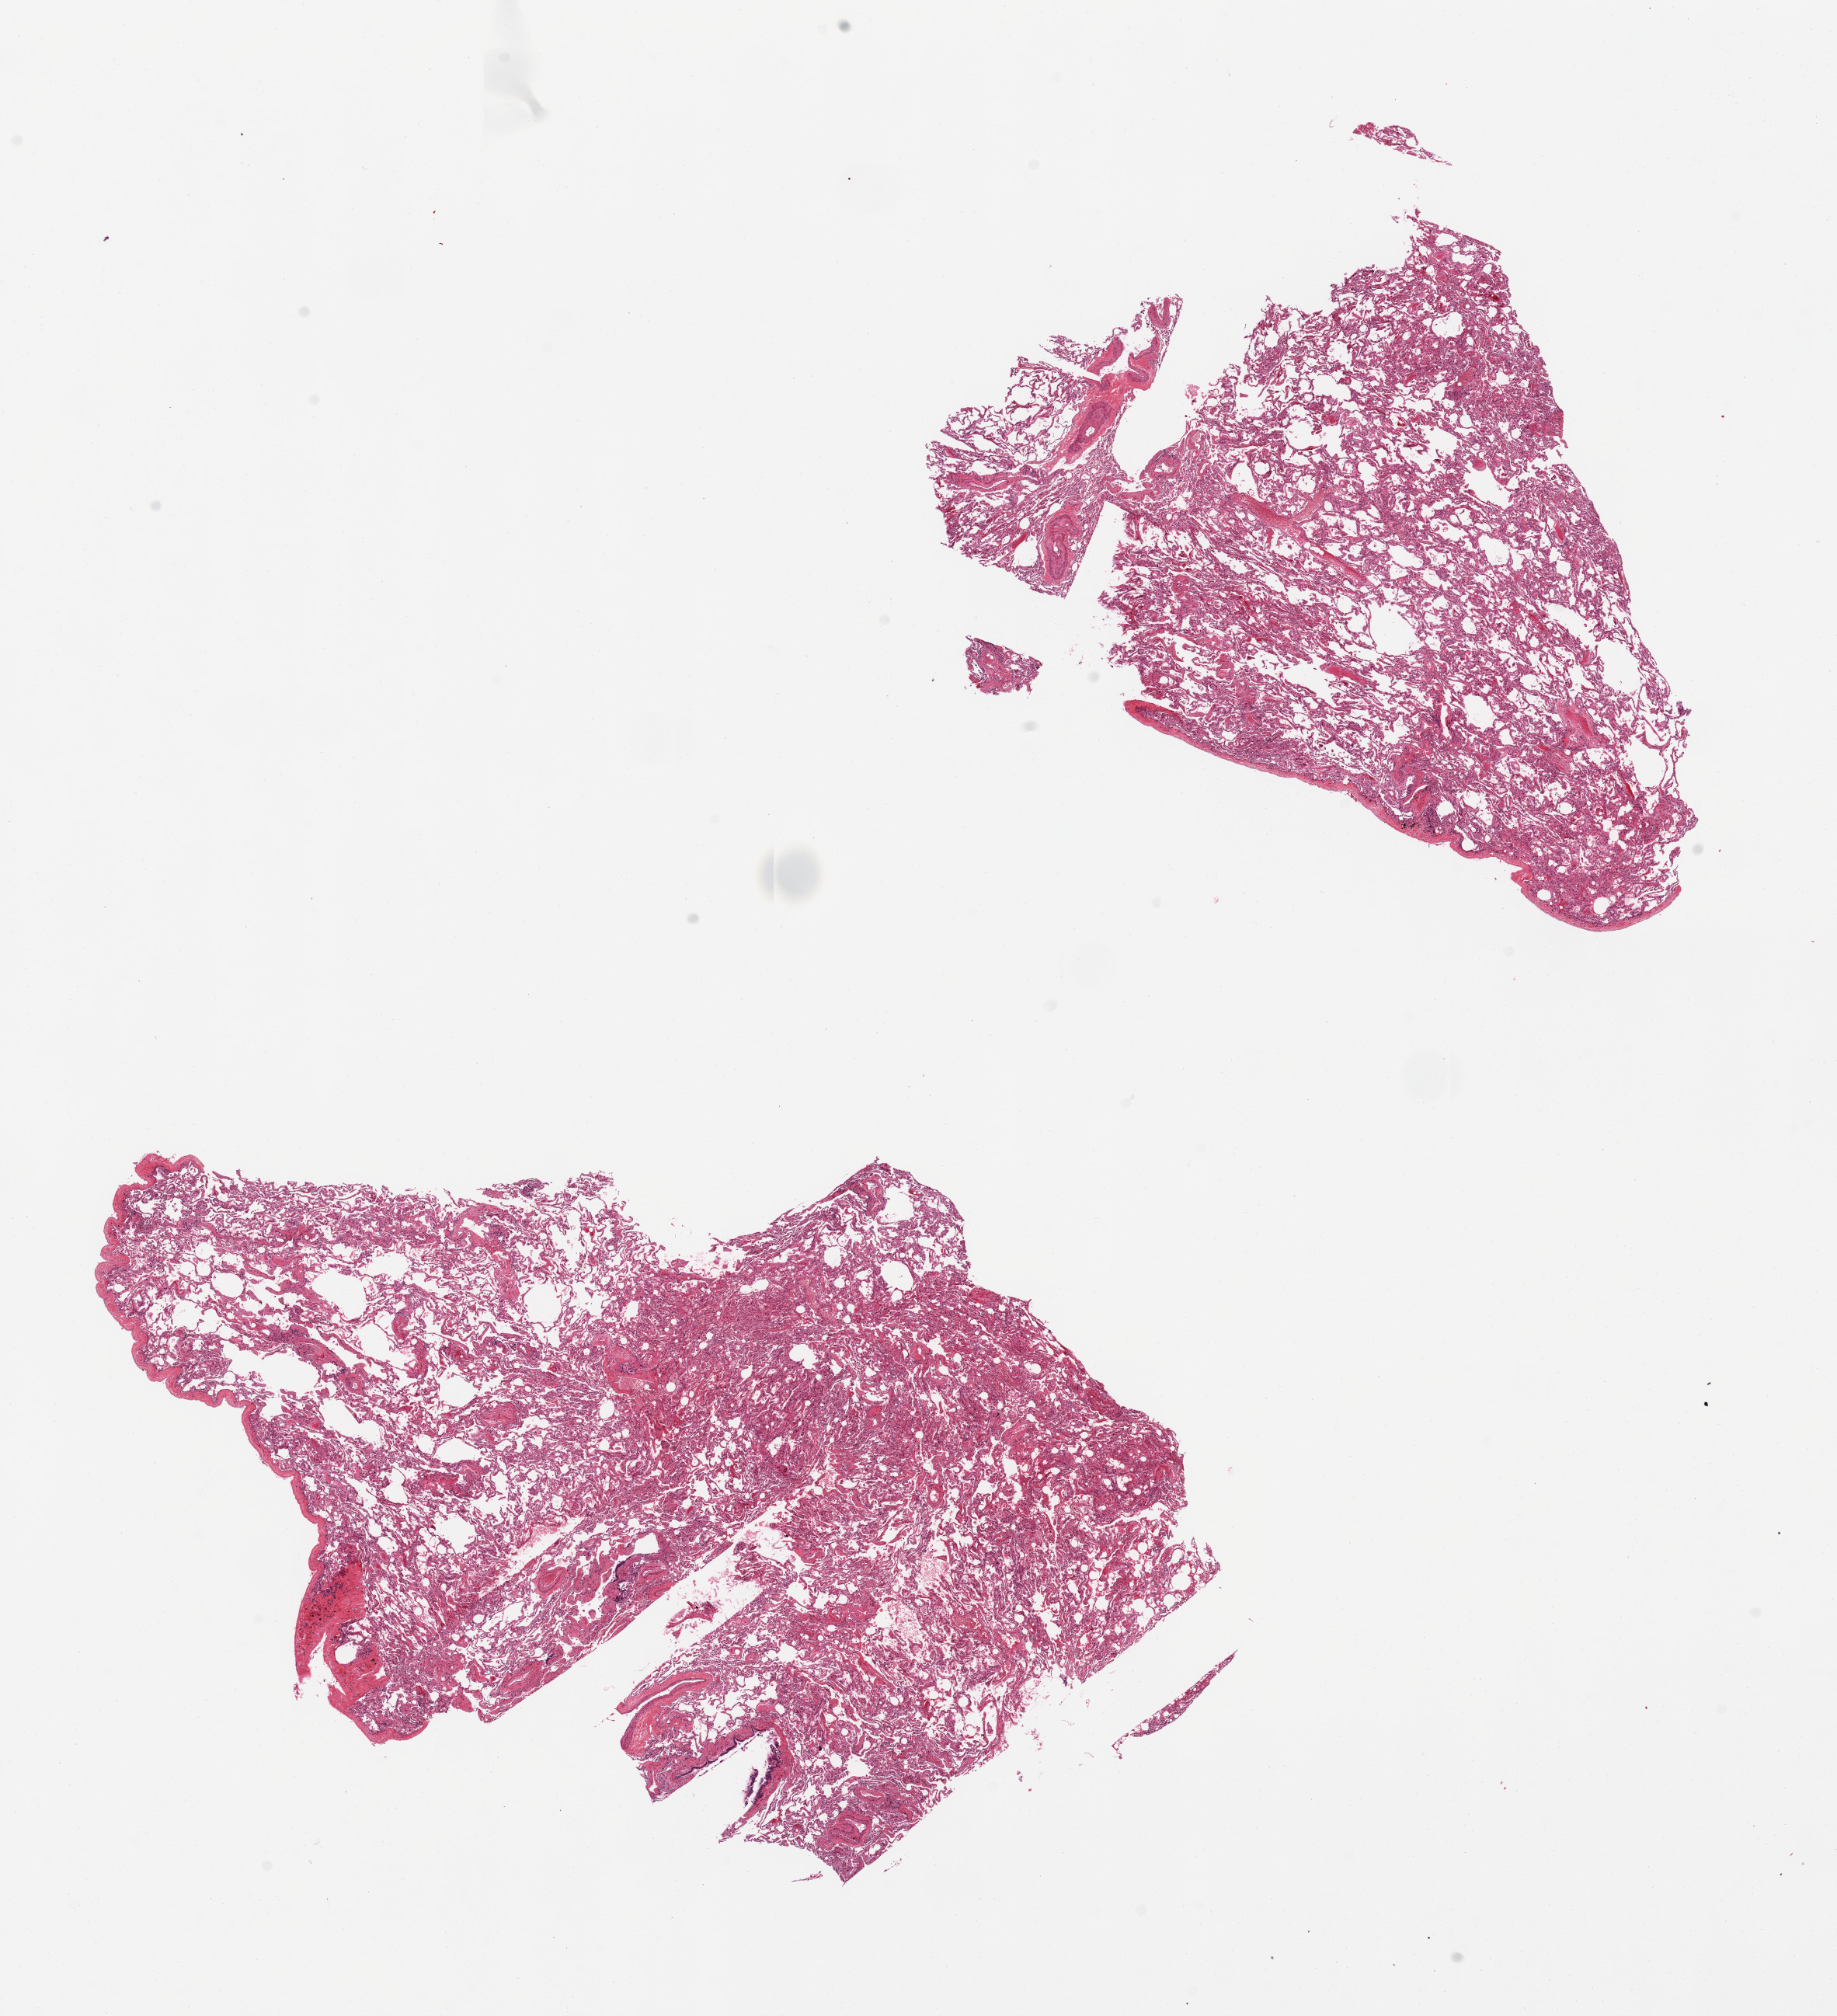
Whole-slide image, H&E stain — low-resolution overview of the scanned area, about 18.7 x 20.5 mm. PAXgene-fixed, paraffin-embedded tissue. Sampled site (target tissue): lung. Donor tissue sample.
Review note (as recorded): 2 pieces; fibrosis. vascular sclerosis; pleura present.